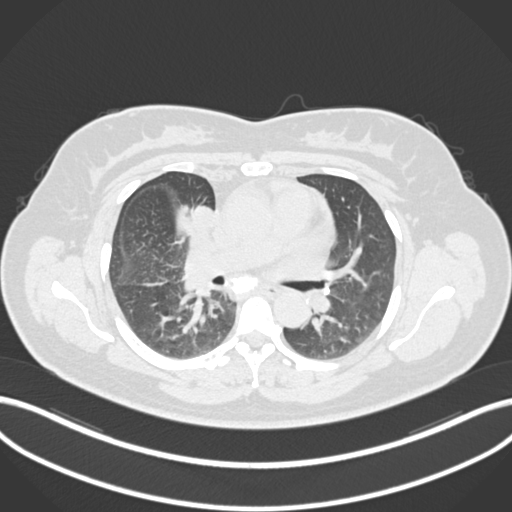
Chest CT, one axial slice; slice 98 of 183 in the series (ordered by position); reconstruction kernel B30f; lung window (W 1500 / L -600 HU); 1 mm slice thickness; 512 × 512 image matrix, field of view 400 × 400 mm. Patient: female, 46 years. Case-level facts recorded for this patient, not image findings: clinical TNM (as recorded): T2a N1 M0.
Outlined on this slice (bounding box drawn by a radiologist):
- lung tumour (recorded histology: adenocarcinoma): bounding box (x1, y1, x2, y2) in pixels: (187, 200, 220, 233)